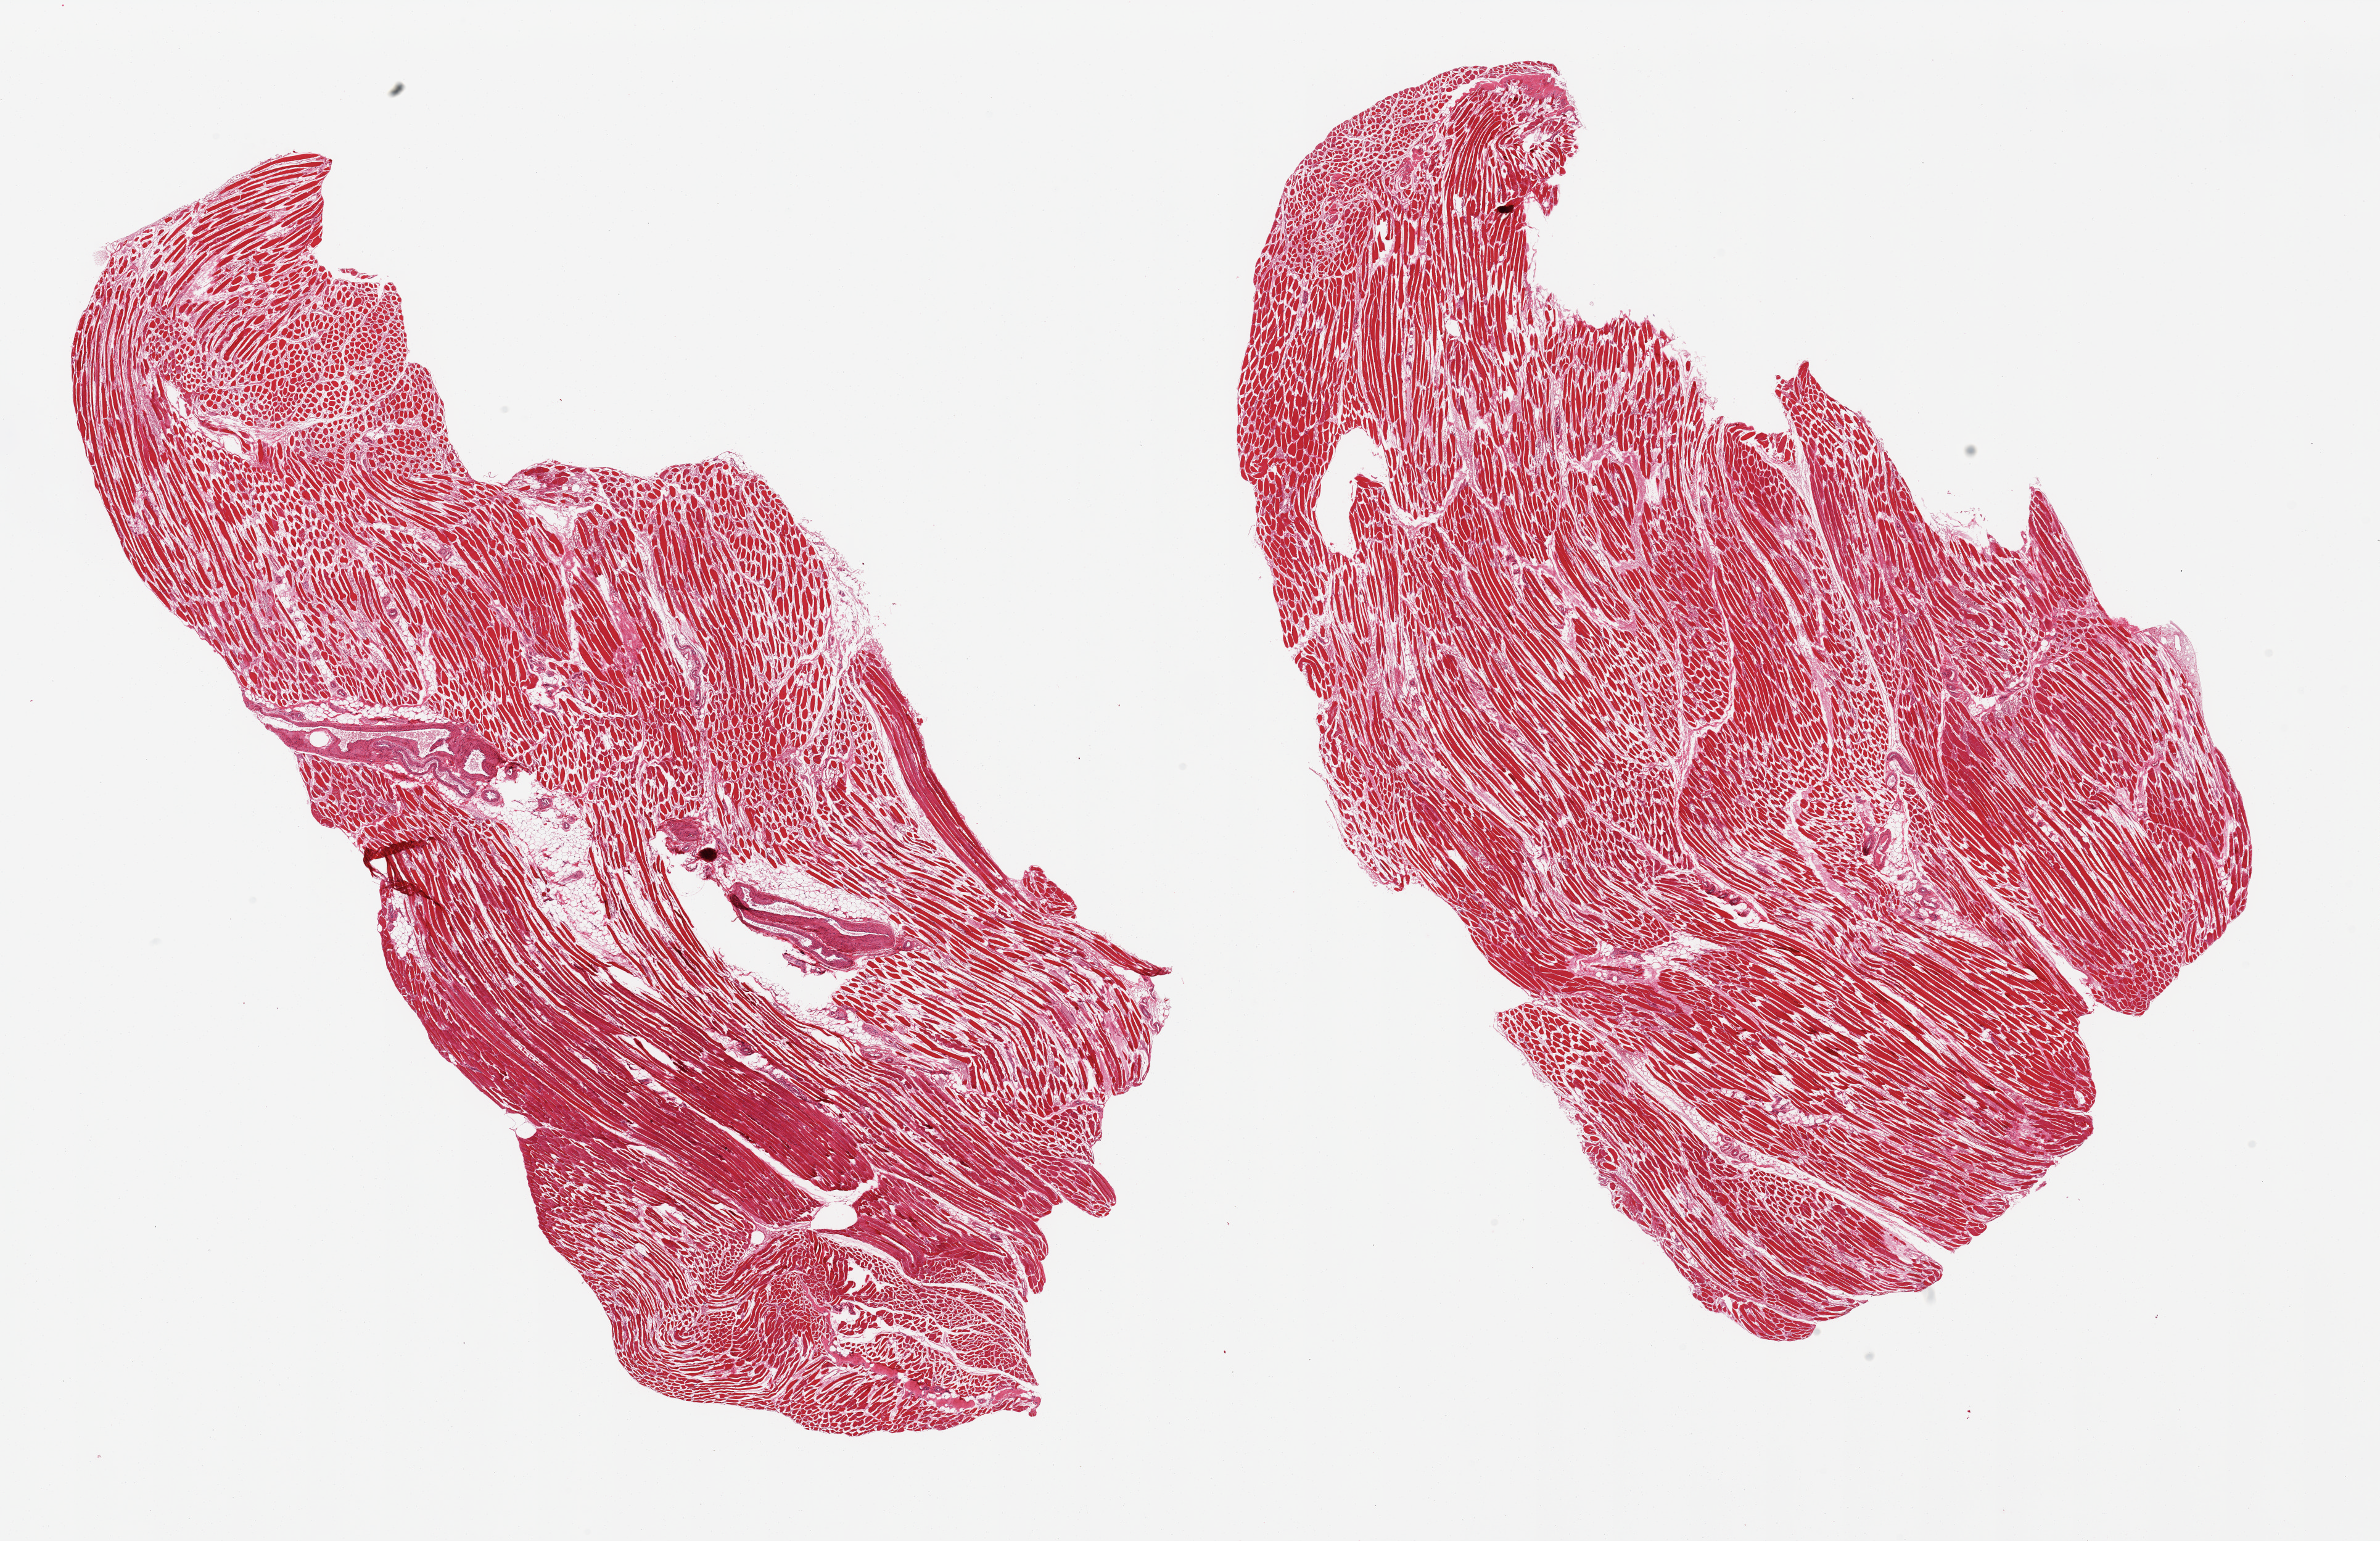
Whole-slide image, H&E stain, shown as a low-resolution overview of the whole scanned area (about 30.5 x 19.8 mm). PAXgene-fixed, paraffin-embedded tissue. Section of skeletal muscle (target tissue). Donor tissue sample. Donor: female.
Reviewer comment on this tissue sample: 2 pieces, atrophic appearing fibers, interstitial fat/vascular elements are ~30-40 %.